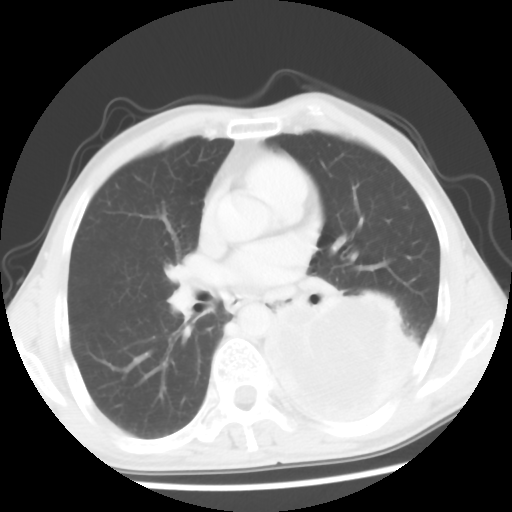
Chest CT, one axial slice. Position 30 of 56 along the scan axis. Reconstruction kernel STANDARD. Lung window (W 1500 / L -600 HU). 5 mm slice thickness. 512 × 512 image matrix. Male patient, age 60 years. Case-level facts recorded for this patient, not image findings: clinical TNM (as recorded): T4 N0 M0.
Outlined on this slice (bounding box drawn by a radiologist):
- lung tumour (recorded histology: squamous cell carcinoma): bounding box (x1, y1, x2, y2) in pixels: (242, 287, 421, 445)